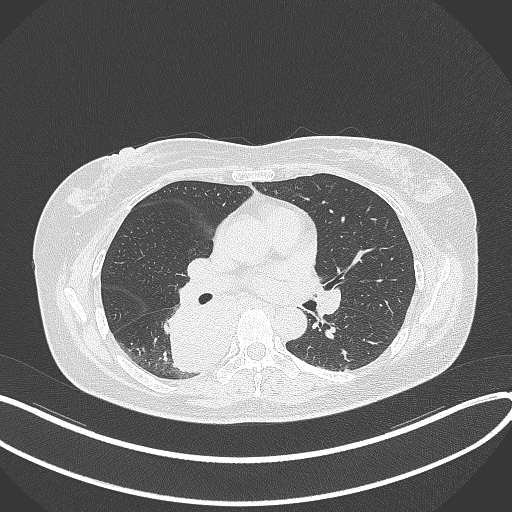
Chest CT, one axial slice; position 197 of 331 along the scan axis; reconstruction kernel B70f; 120 kVp; lung window (W 1500 / L -600 HU); 1 mm slice thickness; 512 × 512 image matrix, field of view 400 × 400 mm. Patient: female, 54 years. From the clinical record (not read from this slice): clinical TNM (as recorded): T4 N0 M0.
Structures marked on this image (rectangle marked by the reading radiologist):
- lung tumour (recorded histology: adenocarcinoma): box from (x=158, y=306) to (x=240, y=375) px